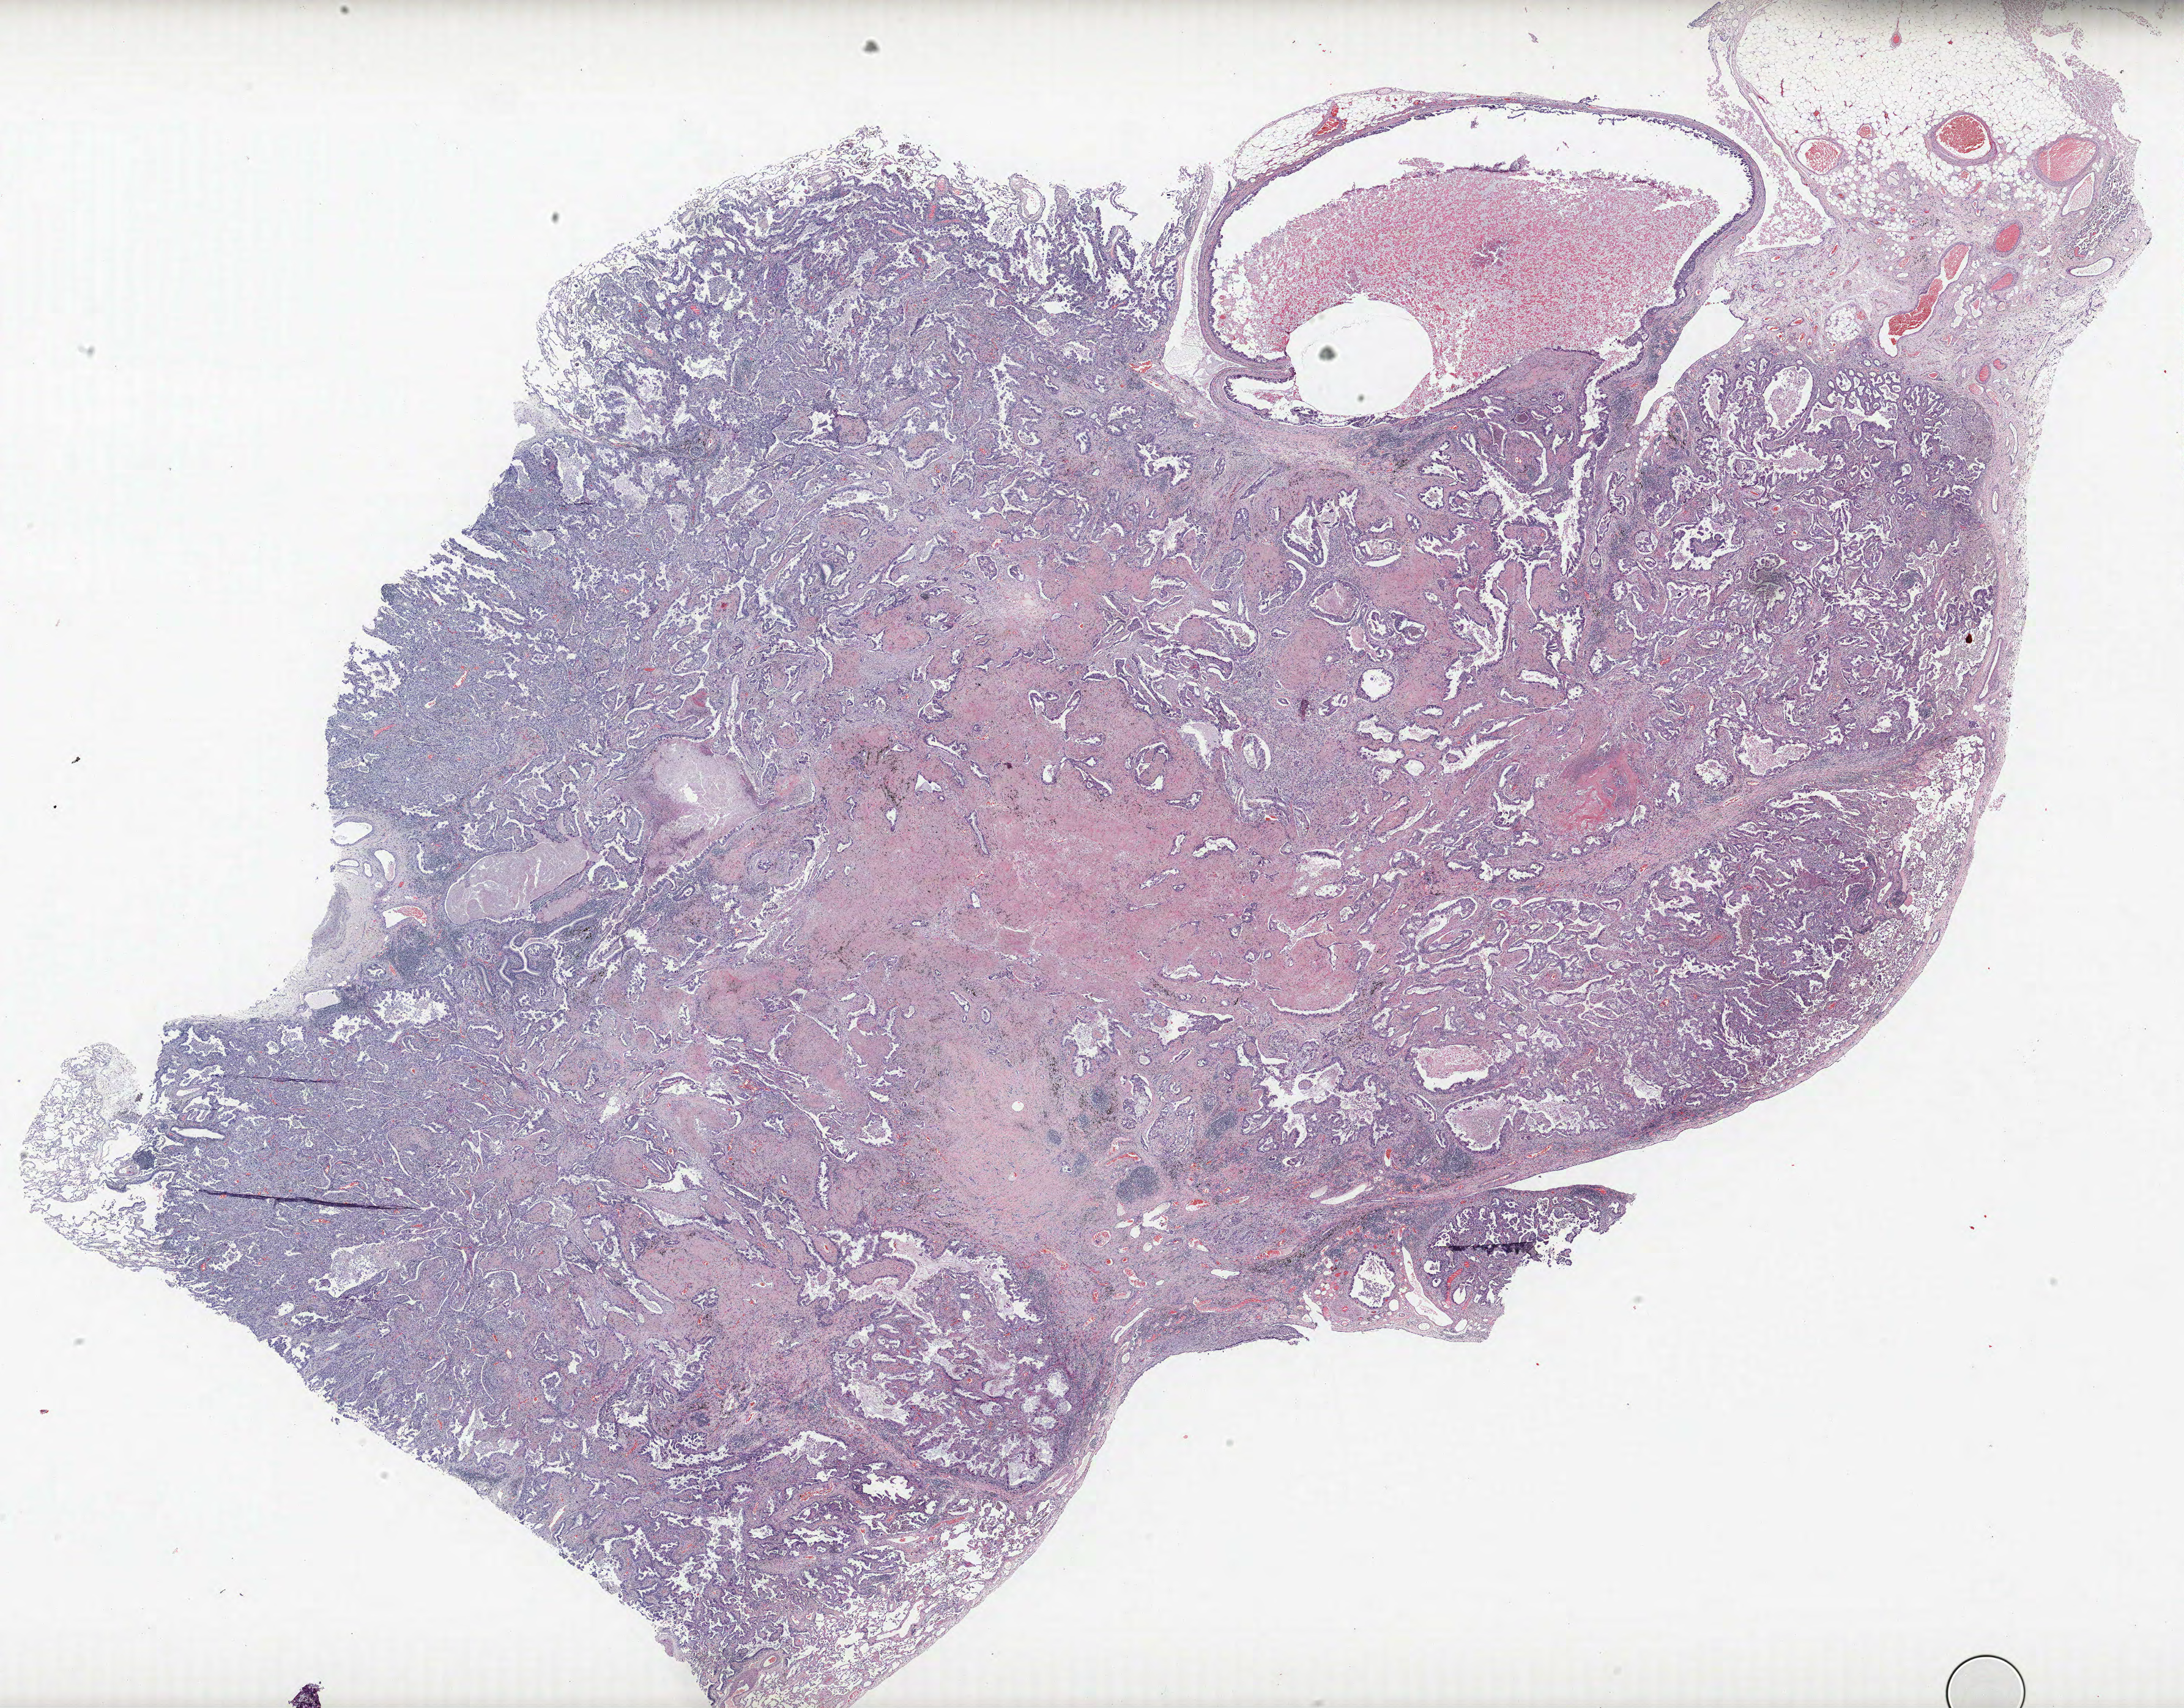
Hematoxylin and eosin (H&E) stained whole-slide image — shown as a low-resolution overview of the whole scanned area (about 28.6 x 22.3 mm, slide scanned at 40x), FFPE section, lung. Male, age 65 at enrolment. Current smoker at enrolment. Grade: poorly differentiated (G3).
Participant's lung-cancer diagnosis: Adenocarcinoma, NOS (ICD-O-3 8140/3). Tumour size (pathology): 25 mm. ICD-O-3 topography: lower lobe of lung (C34.3). Primary tumour location (clinical record): right lower lobe. Stage (AJCC 6th edition): IIIA.